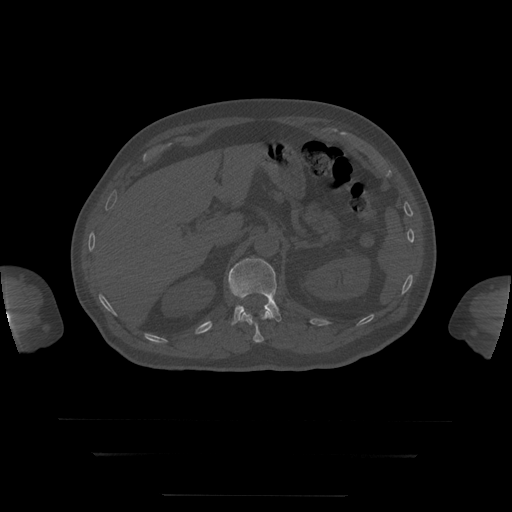
CT including the spine, one axial slice; position 60 of 397 along the scan axis; reconstruction kernel STANDARD; 120 kVp; bone window (W 1800 / L 400 HU); 512 × 512 image matrix, field of view 510 × 510 mm. Patient age 73 years. From the clinical record (not read from this slice): primary cancer: prostate.
Structures marked on this image (semi-automatically segmented with operator editing):
- L1 vertebra: box from (x=229, y=258) to (x=282, y=325) px
- T12 vertebra: (x=240, y=311)–(x=271, y=343)